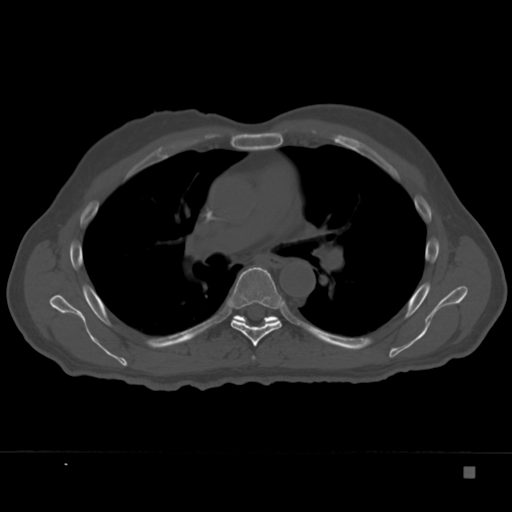
CT including the spine, one axial slice. Slice 237 of 332 in the series (ordered by position). Bone window (W 1800 / L 400 HU). 512 × 512 image matrix. Patient: male, 72 years. From the clinical record (not read from this slice): primary cancer: skeletal.
Structures marked on this image (semi-automatic segmentation, software-assisted and operator-edited):
- T5 vertebra: bounding box <253,356,255,359> (left, top, right, bottom; pixels)
- T6 vertebra: <227,267,285,346>
- T7 vertebra: <232,315,281,326>